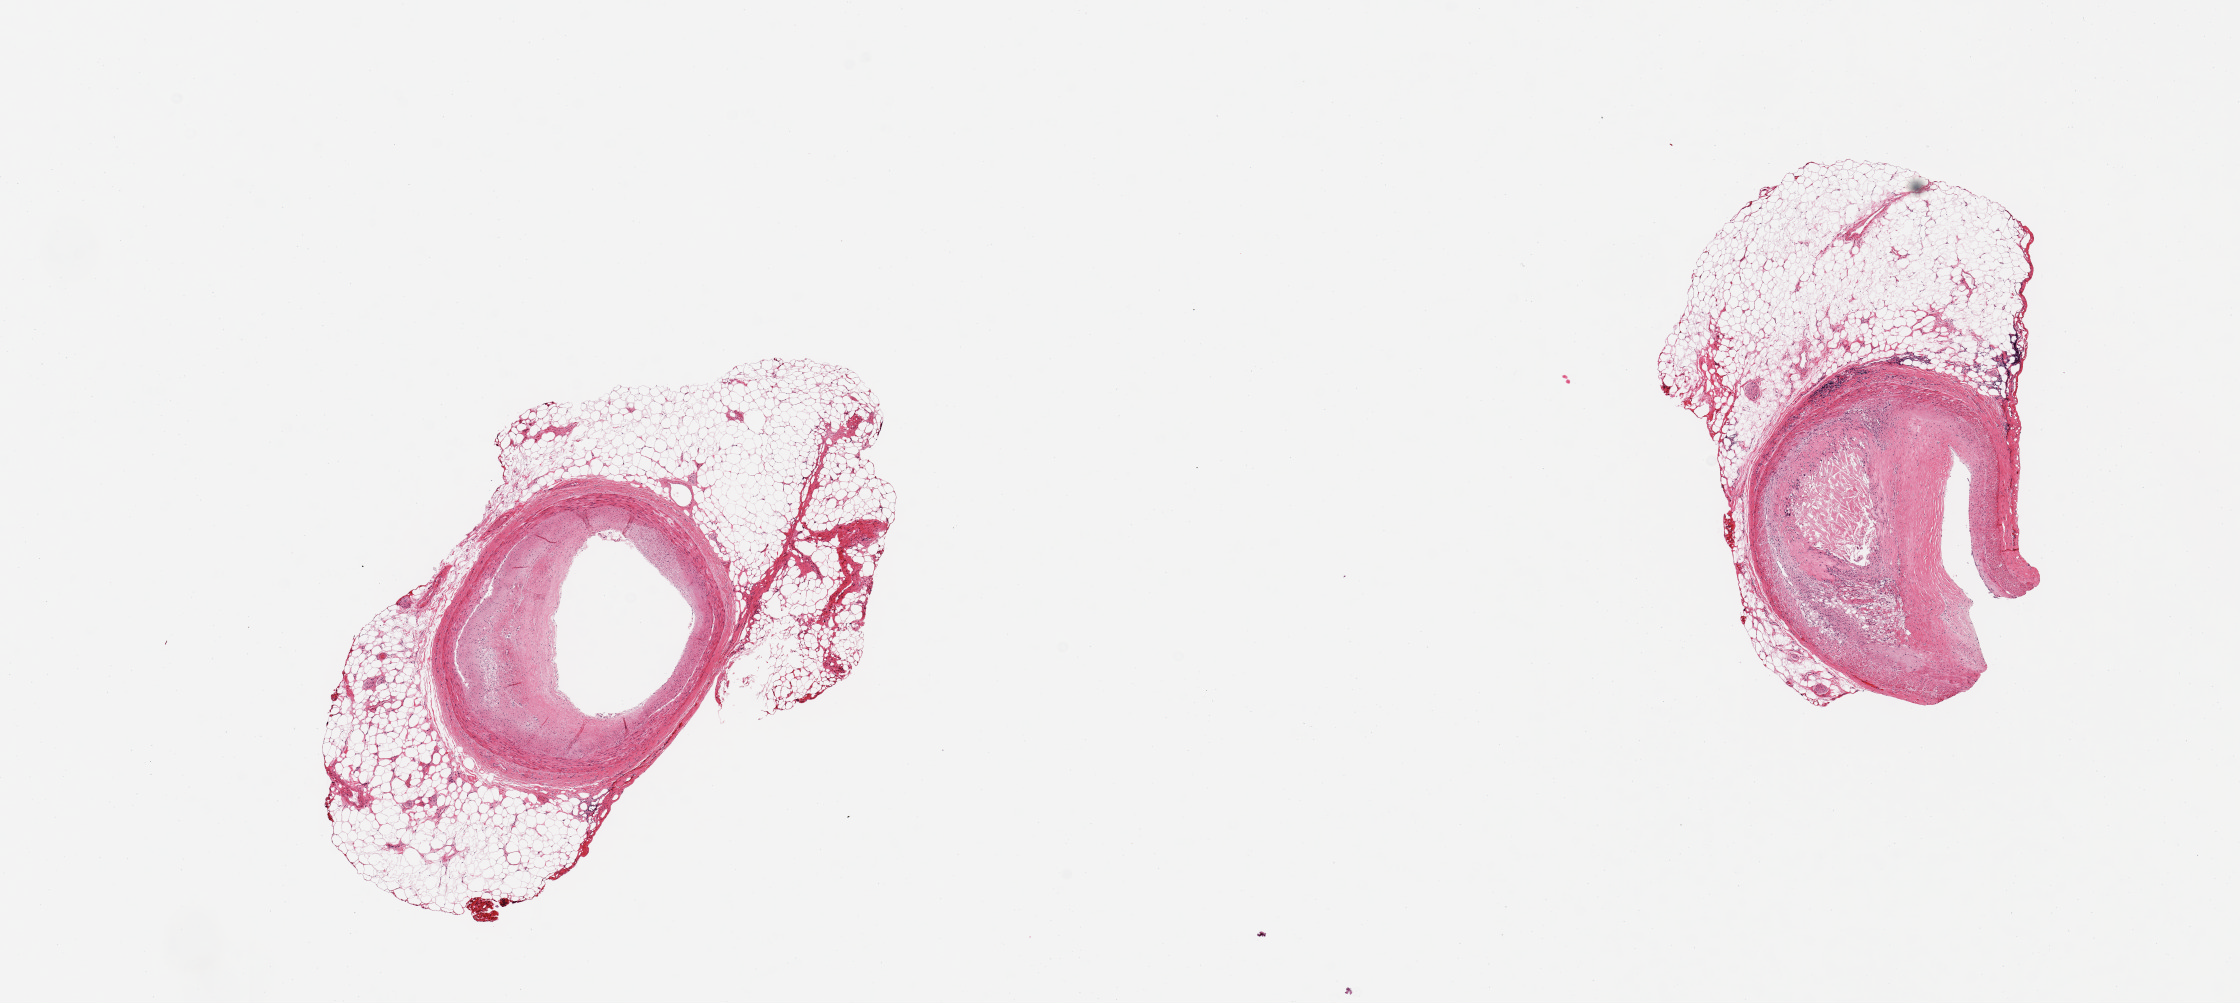
Digitized haematoxylin and eosin-stained section, brightfield — whole scanned area (about 17.7 x 7.9 mm, from a 20x scan) shown as a low-resolution overview. PAXgene-fixed, paraffin-embedded tissue. Target tissue: coronary artery. Tissue donor sample. Donor sex: male.
Review note (as recorded): 2 pieces; atherosclerosis with focal calcification and significant narrowing of the lumen.